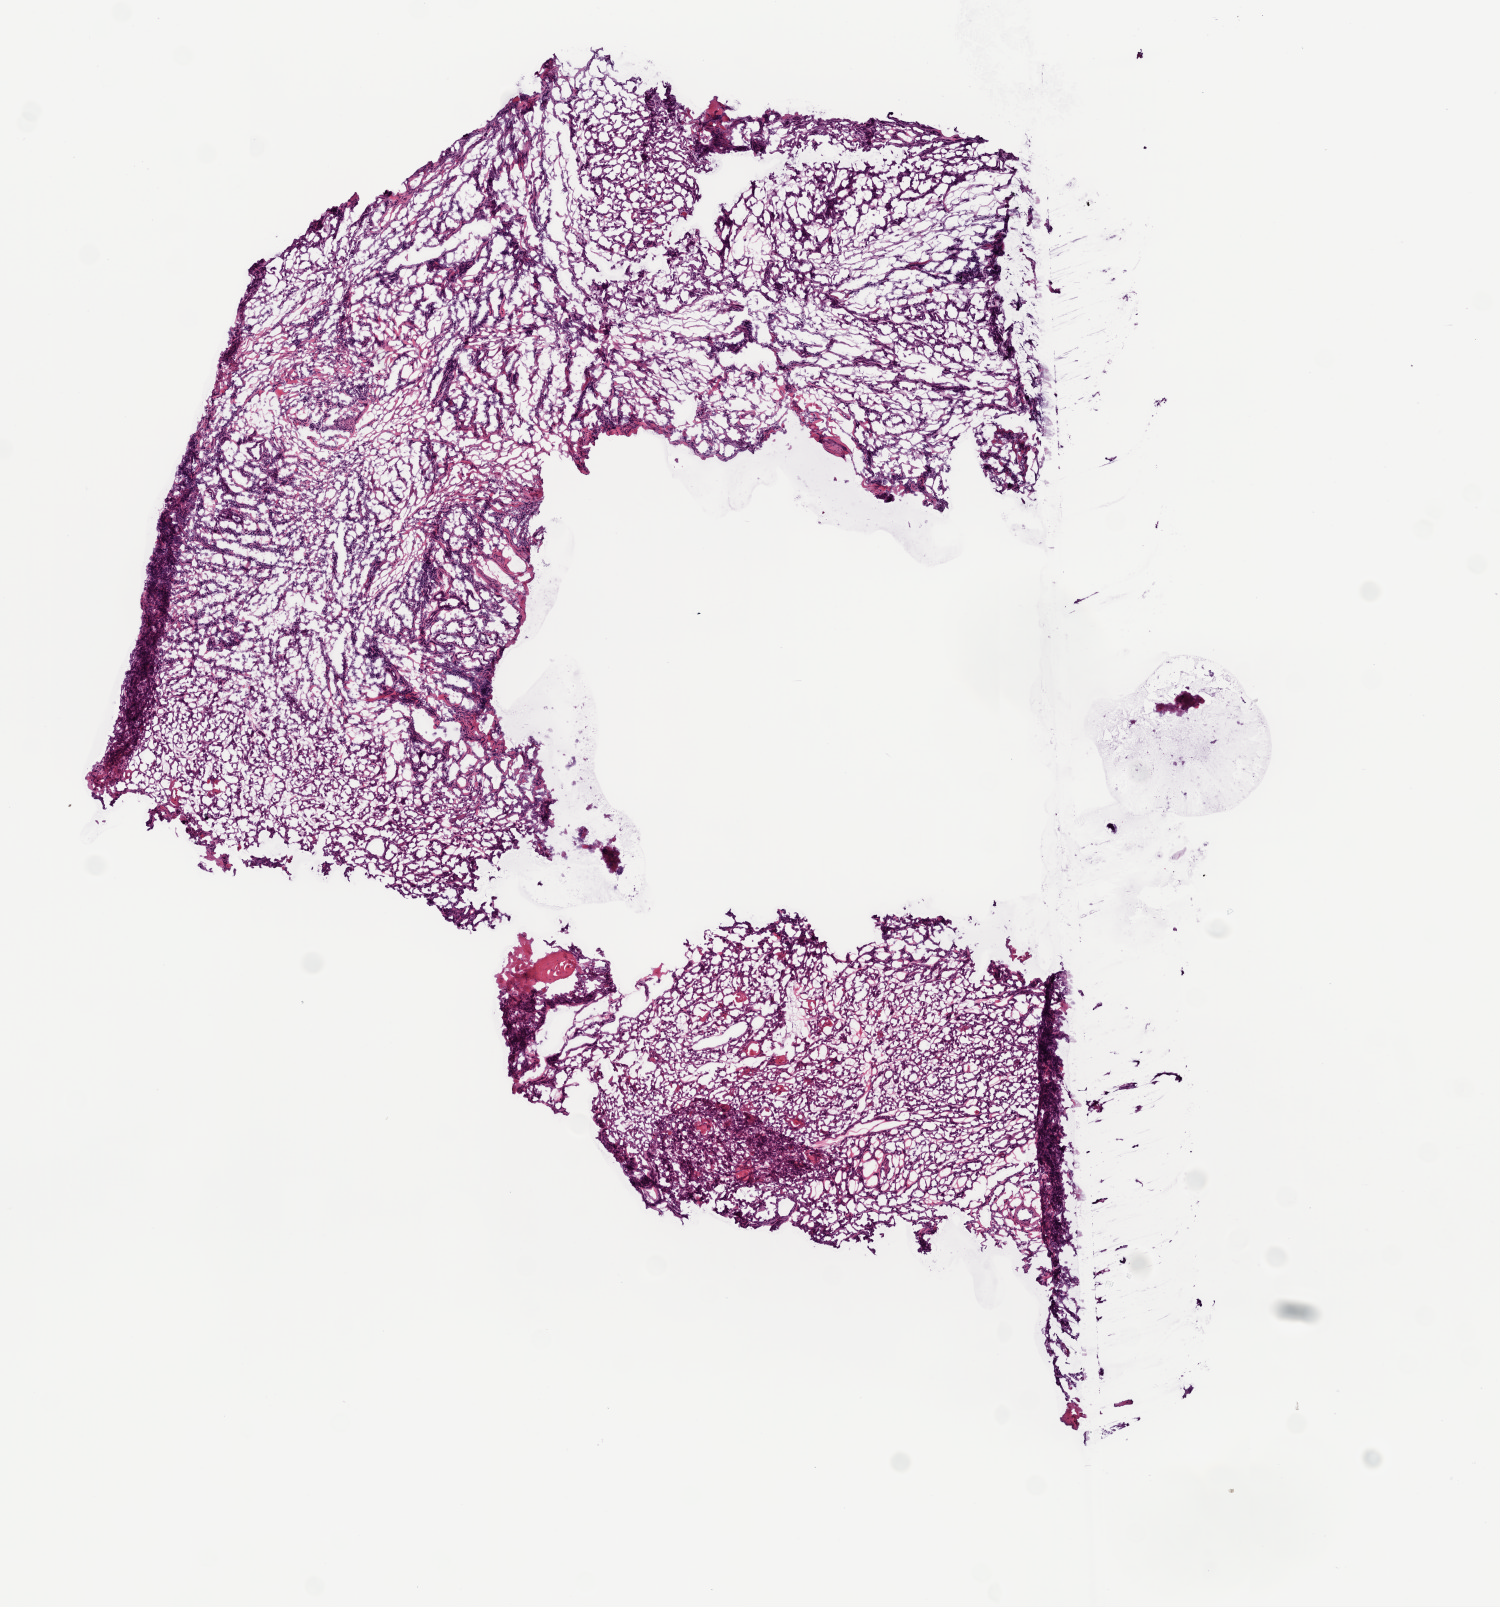
Digitized Hematoxylin and eosin (H&E) stained tissue section (whole slide) — shown as a low-resolution overview of the whole scanned area (about 6.0 x 6.4 mm, slide scanned at 20x), frozen section from the bottom of the tissue portion, primary tumour sample from the head and neck. Male patient; age at initial diagnosis 65 years. Histologic grade: G2 (moderately differentiated). Pathologist review of this section (percent, as recorded): tumour cells 65%, tumour nuclei 50%, normal cells 0%, stromal cells 20%, necrosis 15%.
AJCC pathologic stage: IVA (7th edition). Diagnosis: Squamous cell carcinoma, NOS (floor of mouth, NOS). Lymph nodes positive (case pathology): 6 of 51 examined.